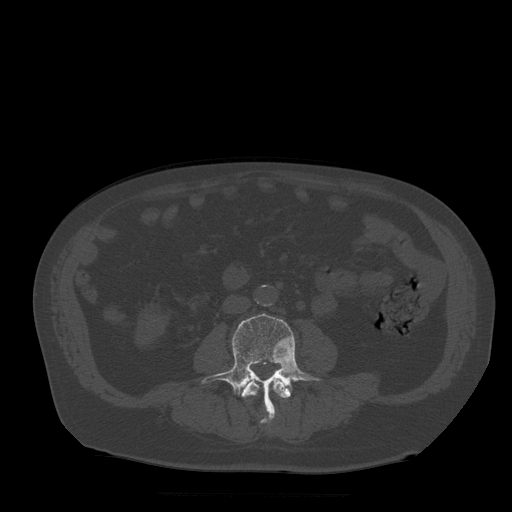
CT including the spine, one axial slice. Slice 120 of 522 in the series (ordered by position). Bone window (W 1800 / L 400 HU). 1.25 mm slice thickness. 512 × 512 image matrix, field of view 420 × 420 mm. Patient age 72 years. From the clinical record (not read from this slice): primary cancer: prostate.
Outlined on this slice (semi-automatically segmented with operator editing):
- L3 vertebra: bounding box (x1, y1, x2, y2) in pixels: (242, 378, 291, 424)
- L4 vertebra: (202, 313, 324, 421)